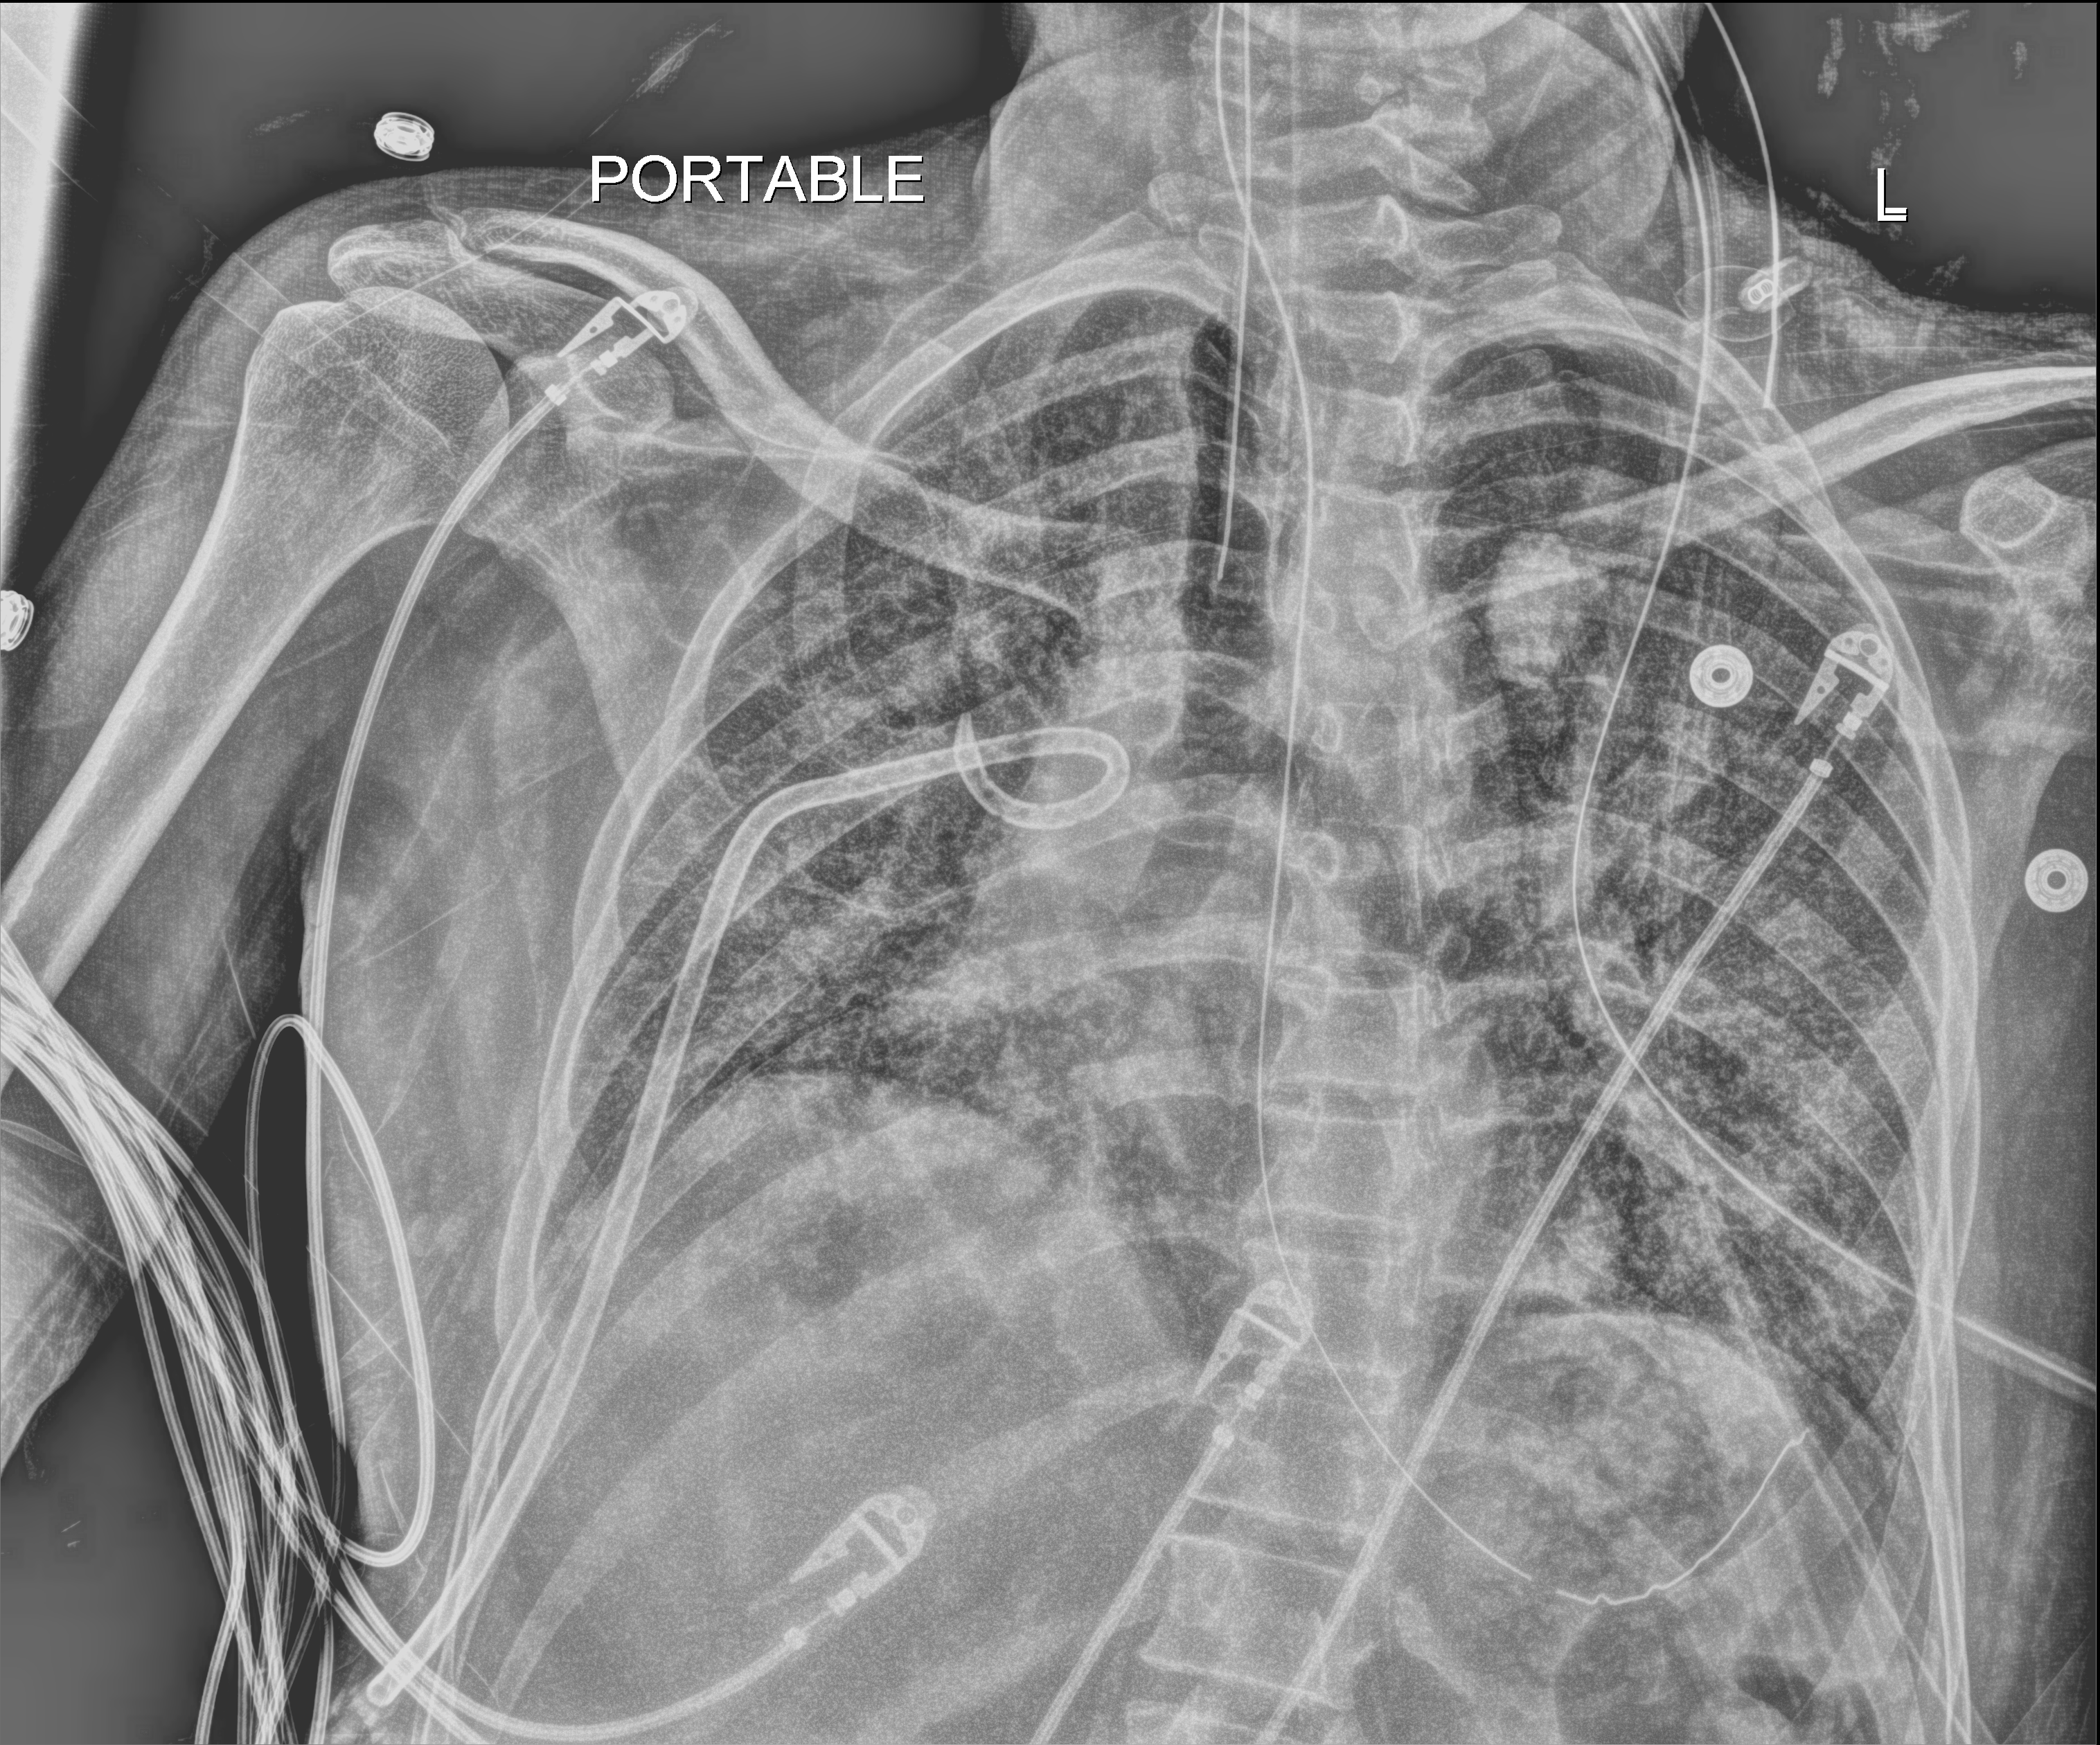
Chest X-ray (portable). Adult patient hospitalised with COVID-19, age 18–59 years.
From the hospital-stay record, not from the radiograph (when in the stay this image was taken is not recorded): mechanically ventilated during this hospital stay: yes; length of hospital stay: 41 days.